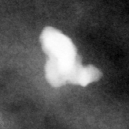
Cropped region of a digitized screen-film mammogram centred on a radiologist-marked abnormality; left breast; CC view.
Marked abnormality: calcifications, morphology round and regular / lucent center / dystrophic, distribution diffusely scattered; BI-RADS assessment category 2; benign; no additional work-up was recommended (benign without callback).